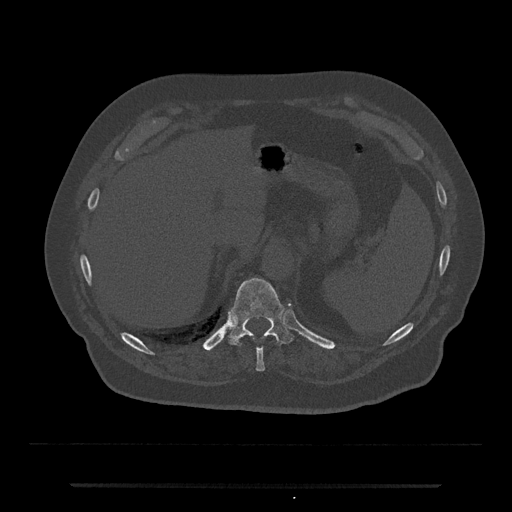
CT including the spine, one axial slice. Slice 666 of 797 in the series (ordered by position). 120 kVp. Bone window (W 1800 / L 400 HU). 512 × 512 image matrix, field of view 434 × 434 mm. Male patient, age 80 years. Case-level facts recorded for this patient, not image findings: primary cancer: prostate; vertebrae with lytic lesions (as recorded): L1, T11.
Outlined on this slice (semi-automatic segmentation, software-assisted and operator-edited):
- T10 vertebra: bounding box (x1, y1, x2, y2) in pixels: (256, 348, 265, 371)
- T11 vertebra: (227, 278, 294, 346)